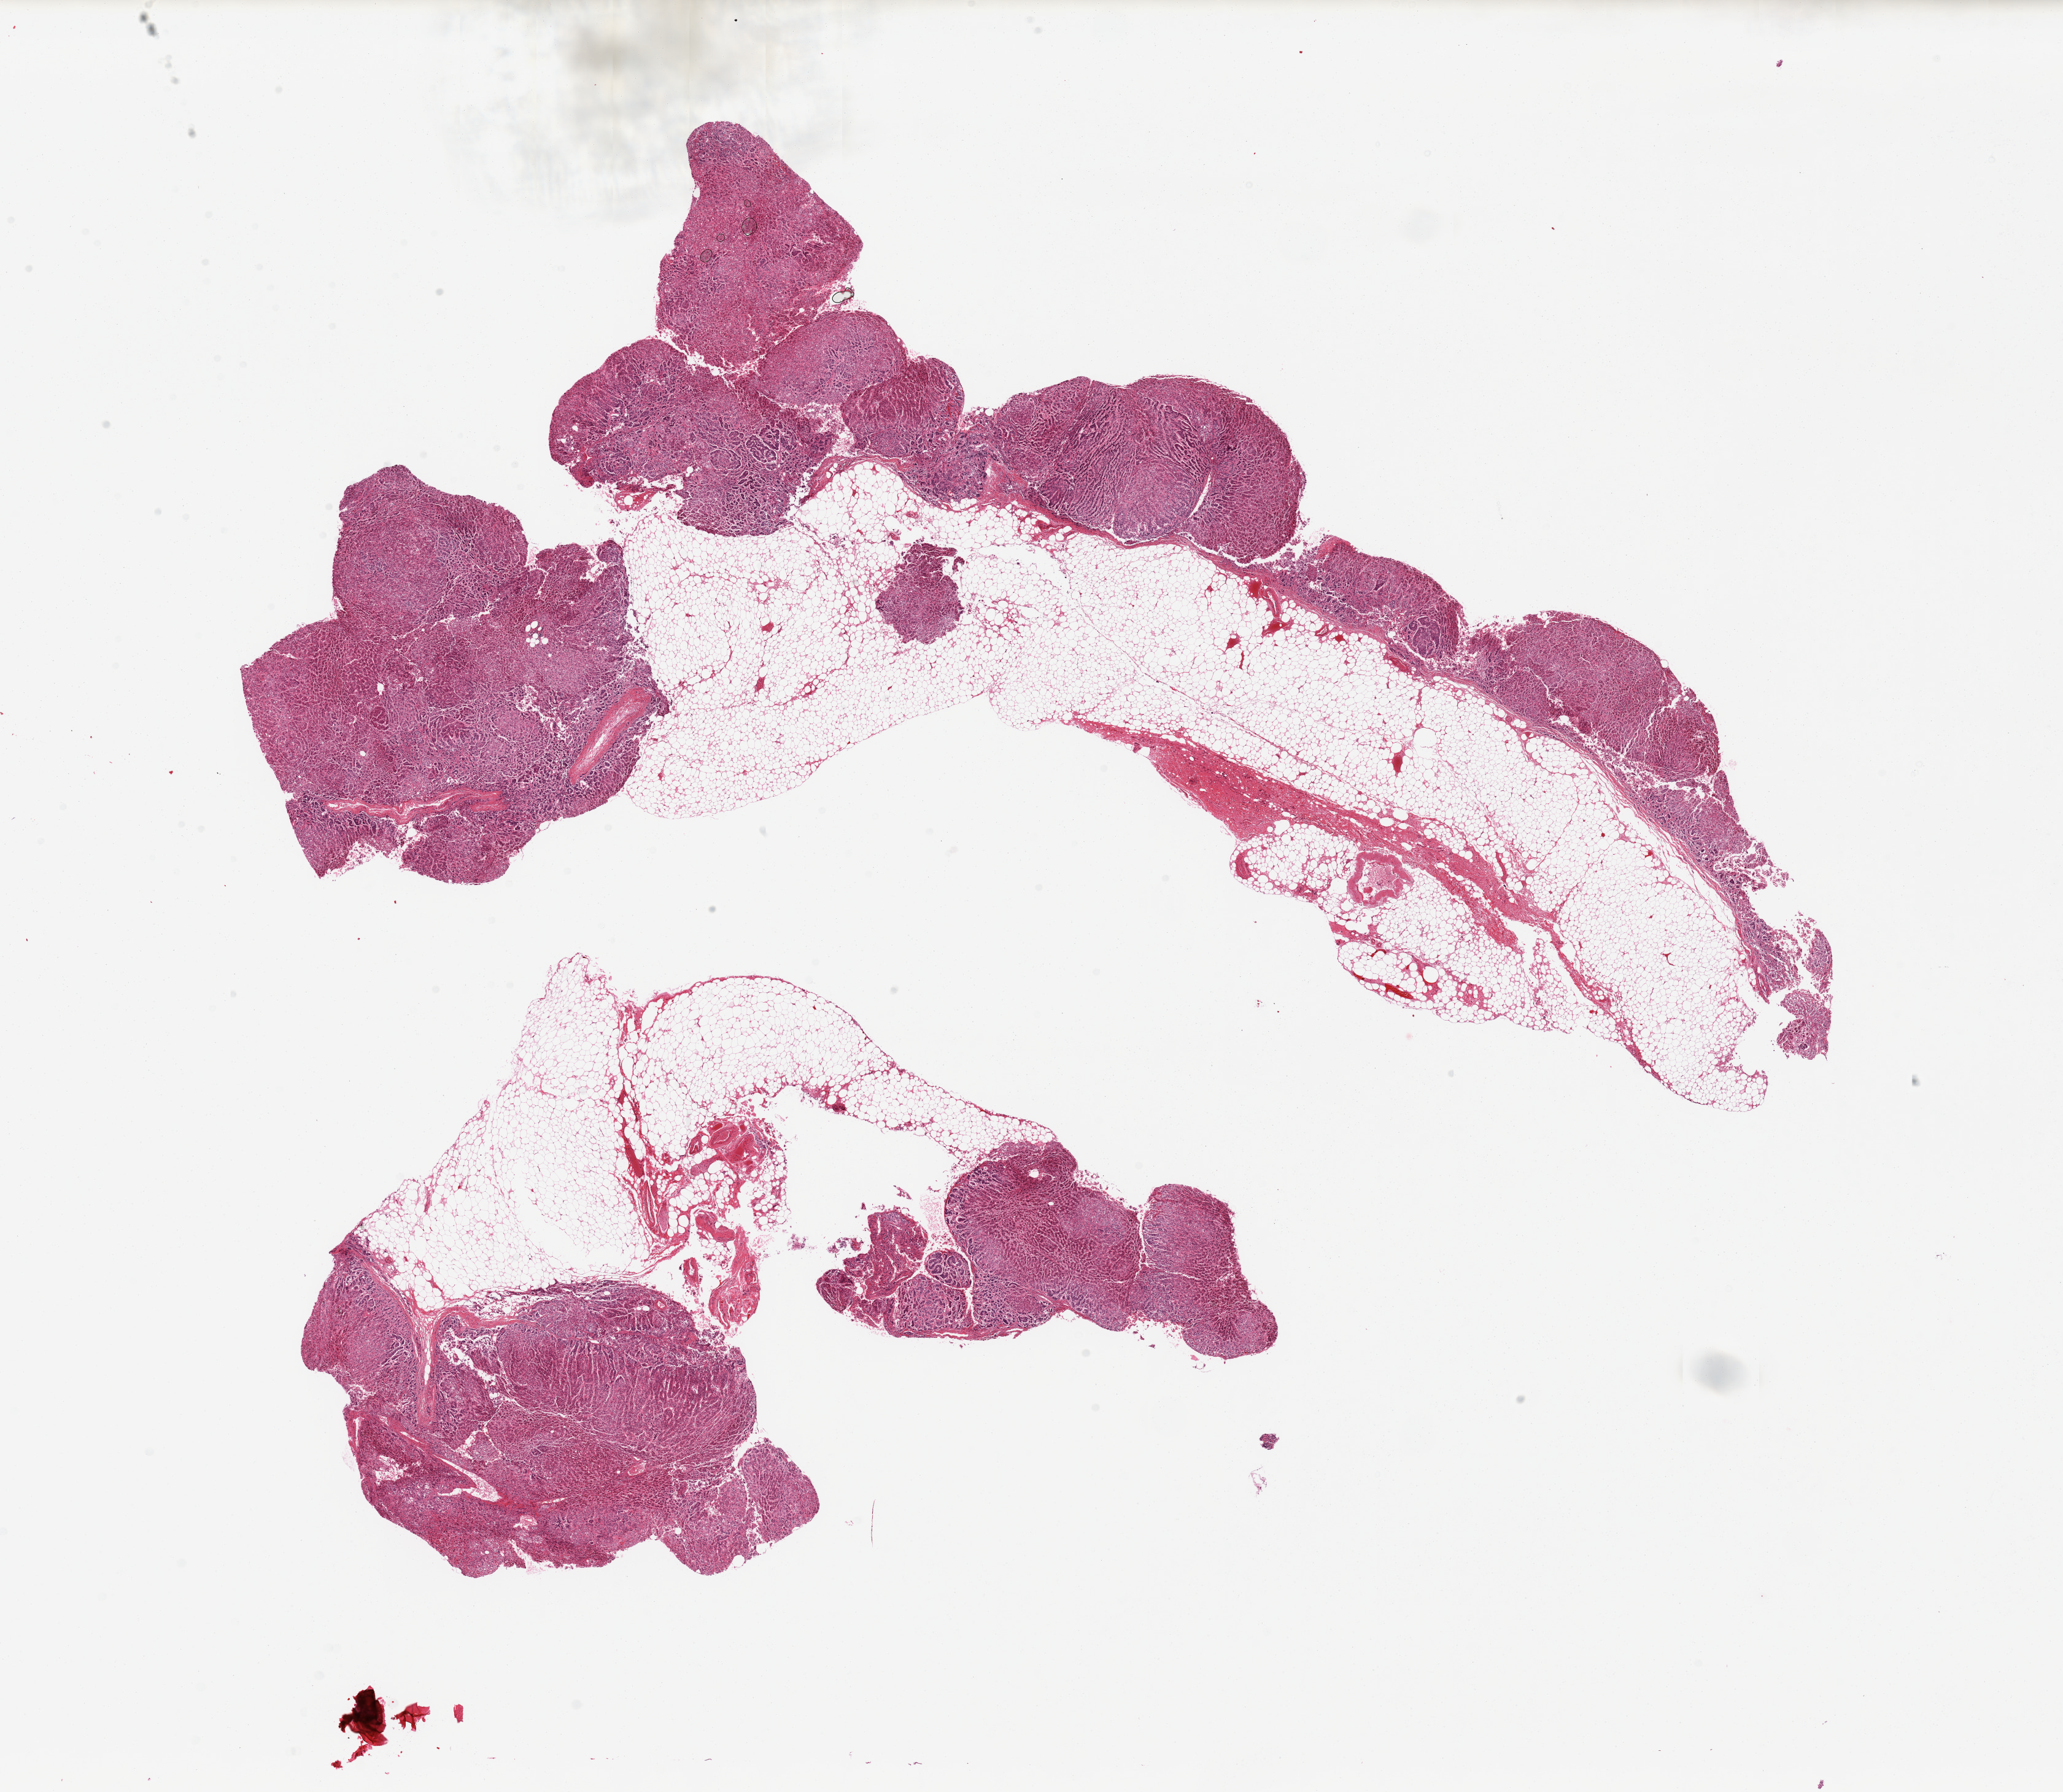
H&E whole-slide image, whole scanned area (about 26.6 x 23.1 mm, from a 20x scan) shown as a low-resolution overview. PAXgene-fixed, paraffin-embedded tissue. Target tissue: adrenal gland. Tissue donor sample. Donor: female.
Reviewer comment on this tissue sample: 2 pieces, ~50% is attached fat.